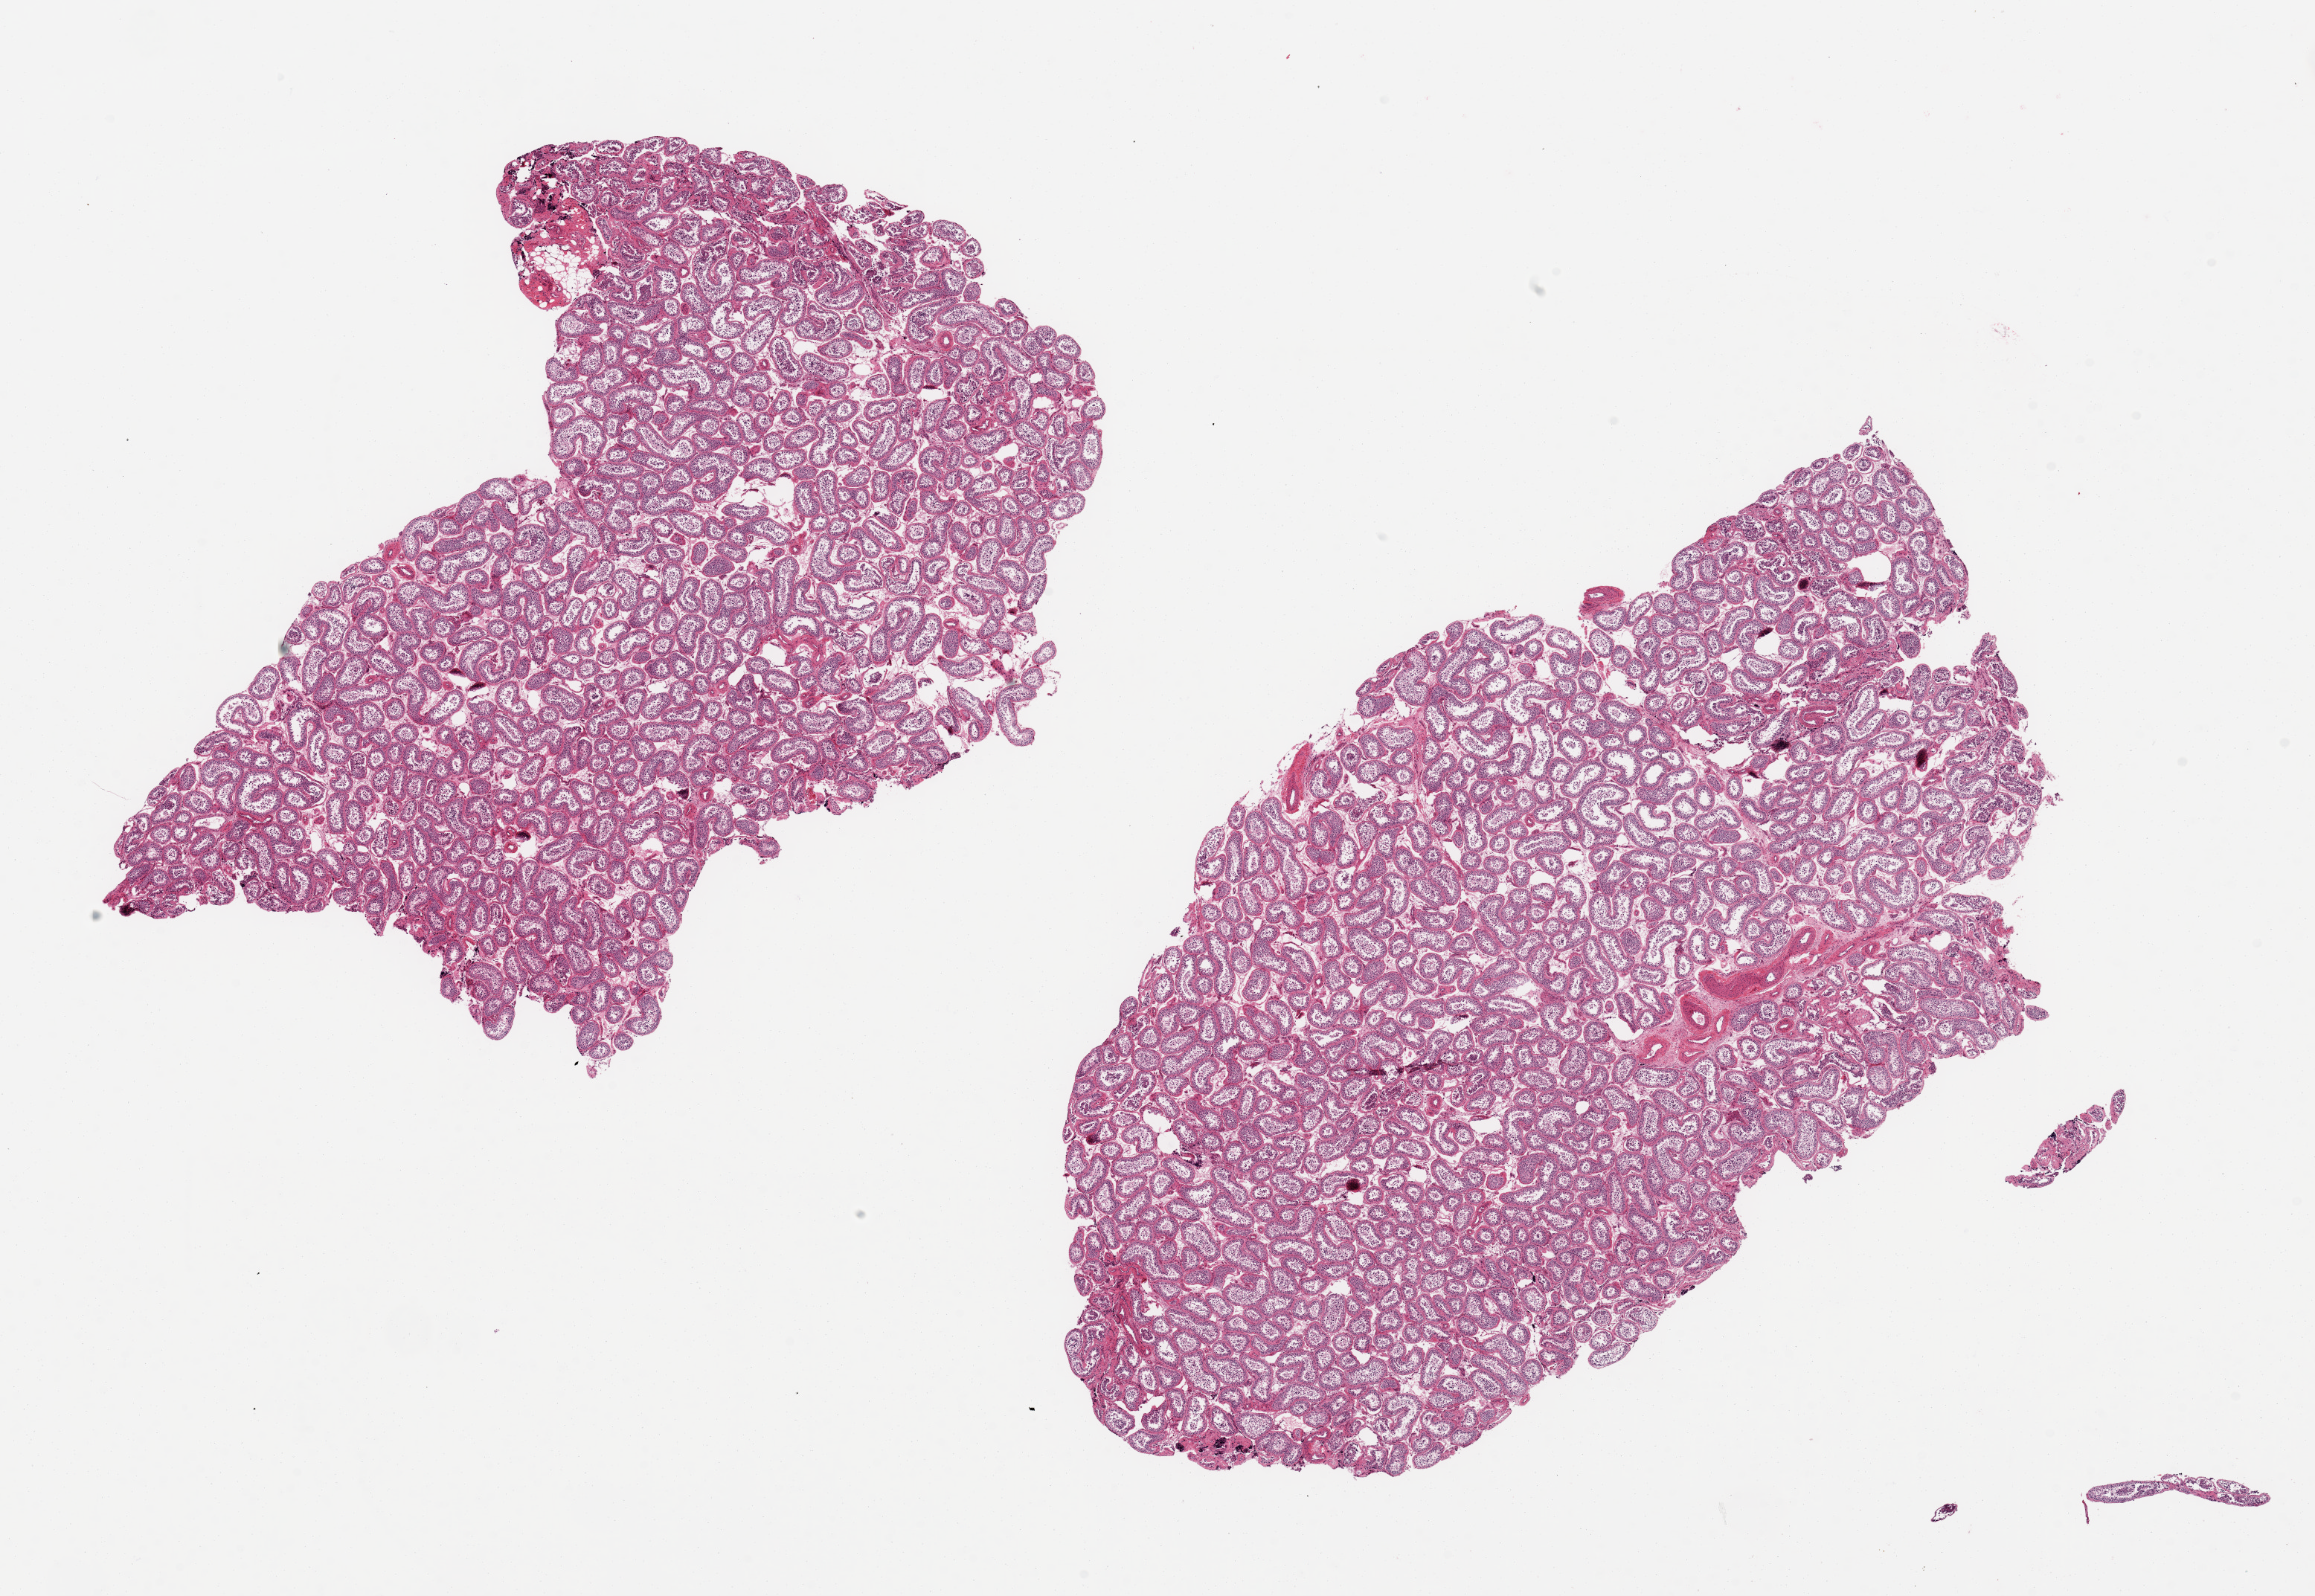
Haematoxylin and eosin whole-slide image, brightfield — a low-resolution overview of the entire scanned area, about 24.6 x 17.0 mm (from a 20x scan); PAXgene-fixed paraffin-embedded (PFPE) section; sampled site (target tissue): testis; donor tissue sample. Male donor.
Reviewer comment on this tissue sample: 2 aliquots ~11x6mm. Spermatogenesis reduced but present.